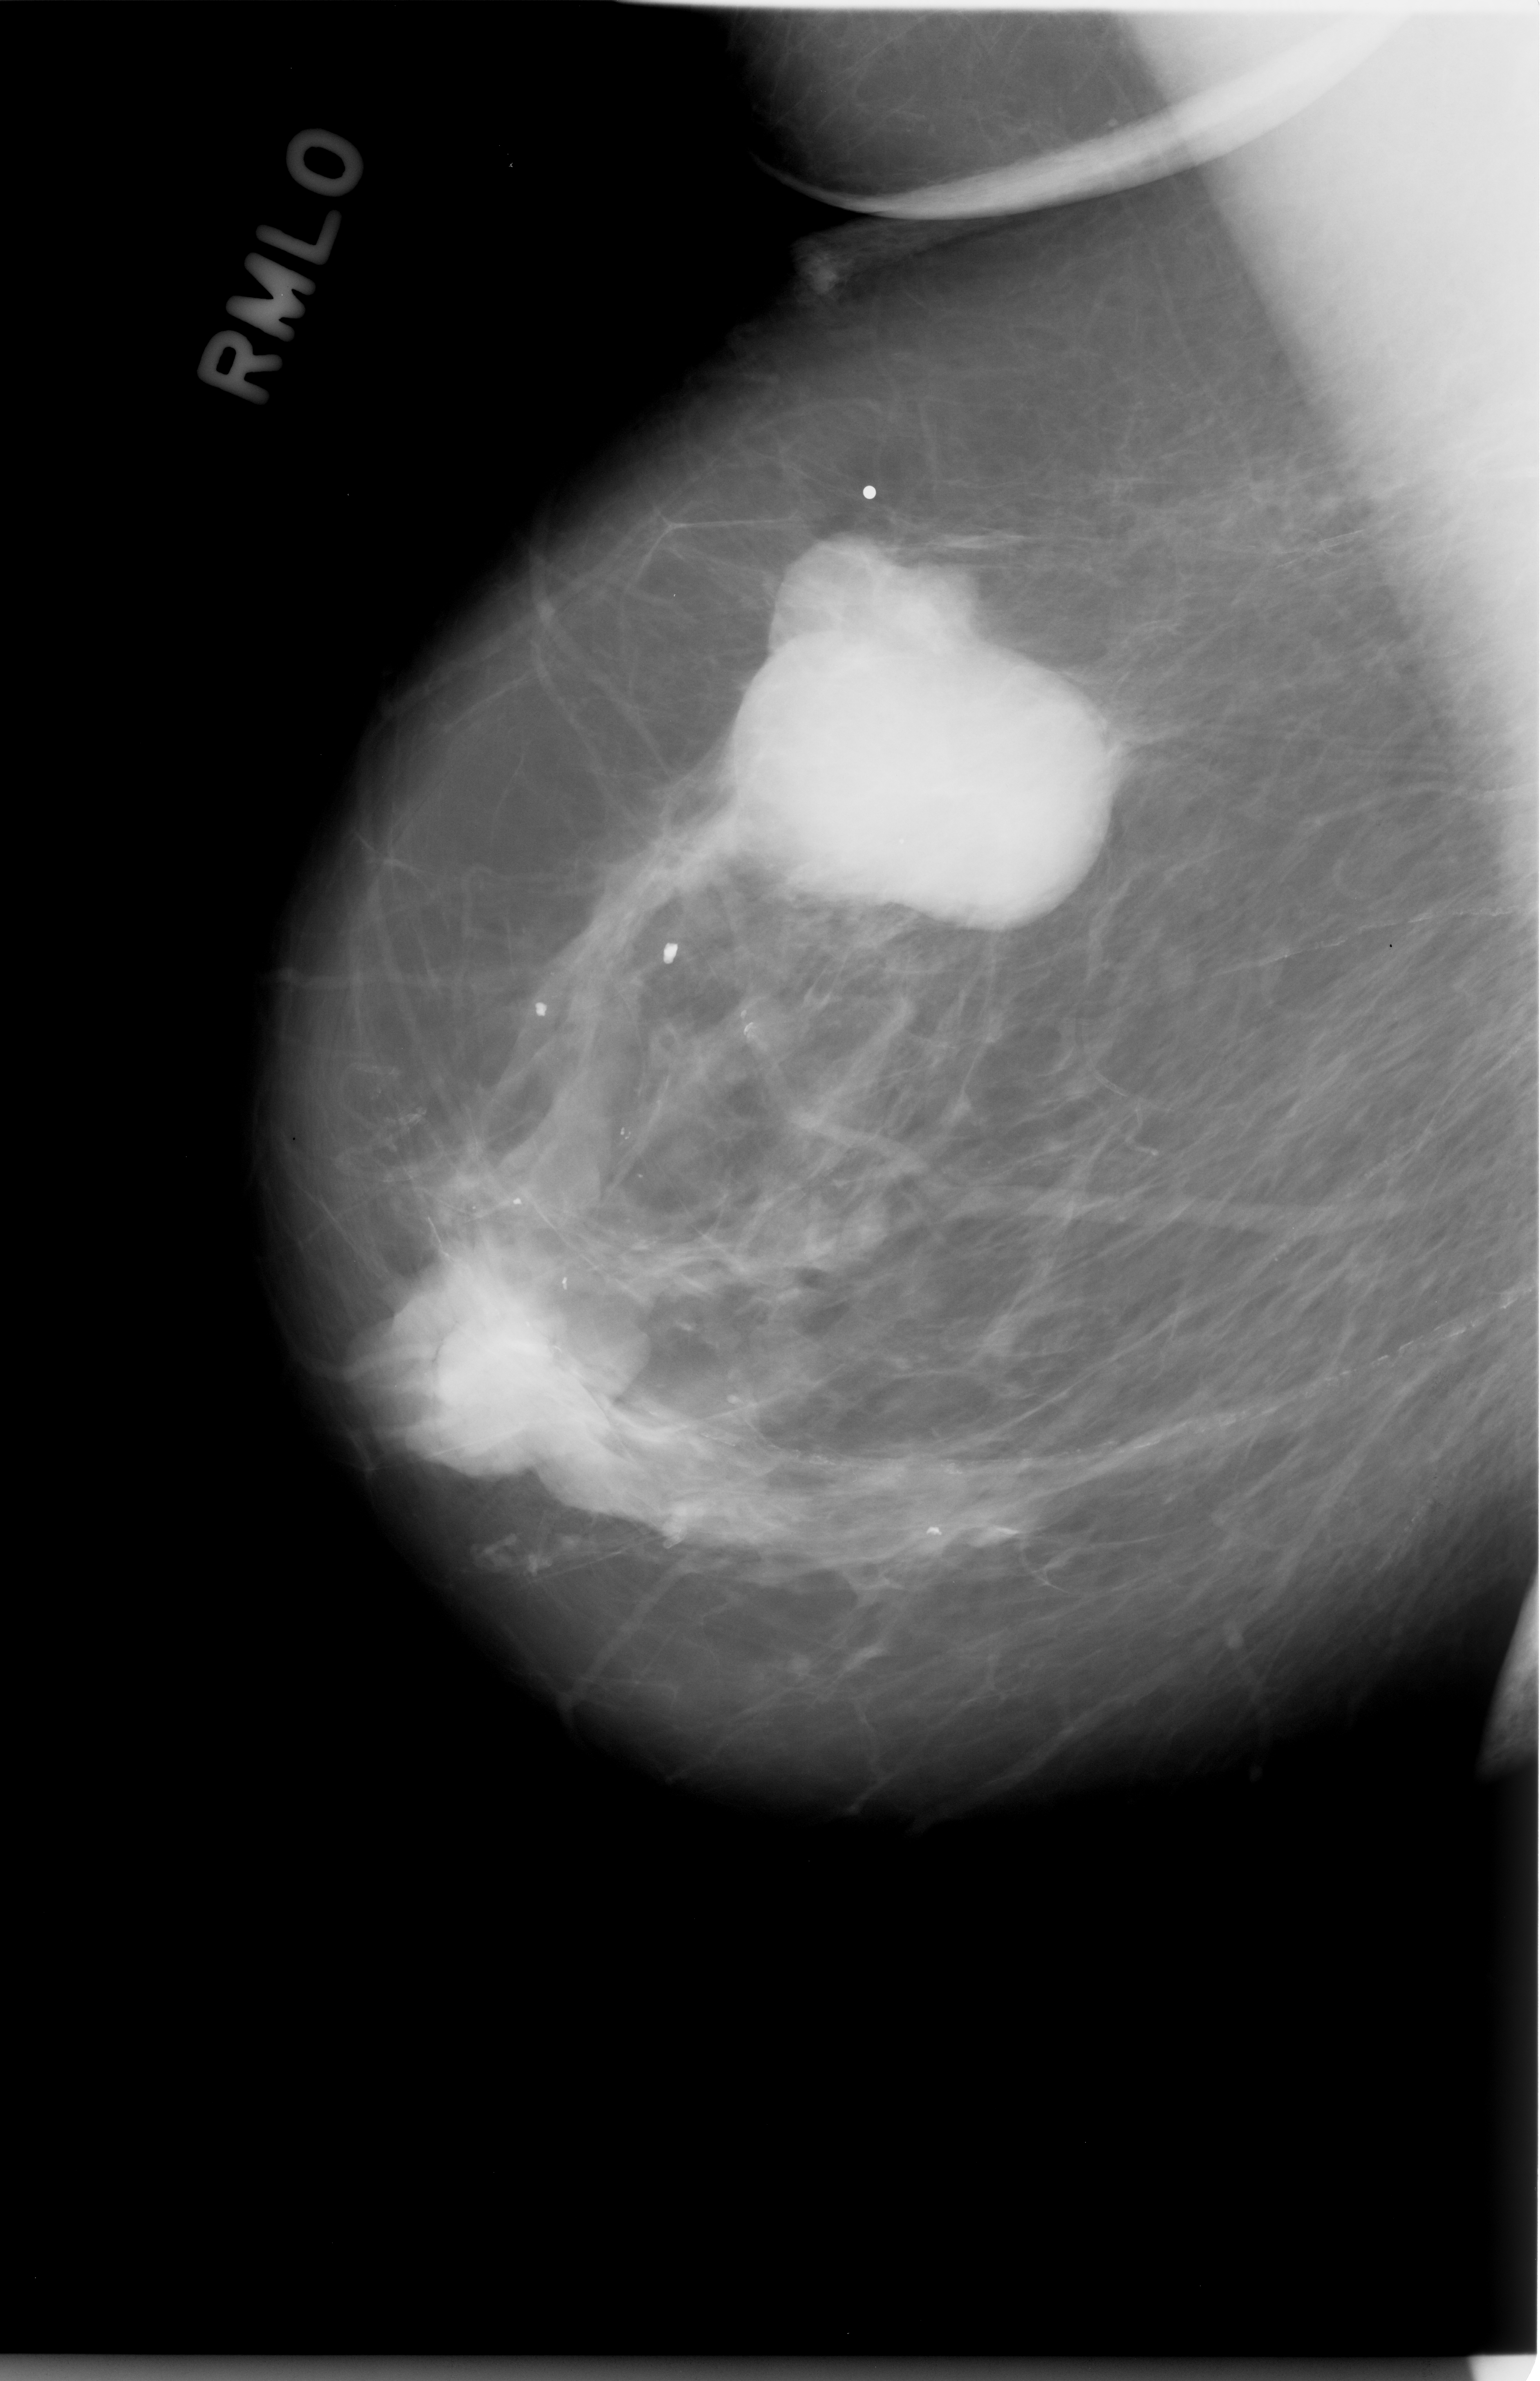
Mammogram (digitized film); right breast; mediolateral oblique (MLO) view; breast composition: almost entirely fatty (BI-RADS density category 1 of 4); 1540 × 2381 image matrix.
Expert-marked regions of interest on this film, with their recorded descriptors:
- Finding 1 of 2: mass, shape lobulated, margins circumscribed; BI-RADS assessment category 5; pathology result (as recorded, not read from the image): malignant: bounding box (x1, y1, x2, y2) in pixels: (343, 1192, 634, 1566)
- Finding 2 of 2: mass, shape lobulated, margins circumscribed; BI-RADS assessment category 5; subtlety rating 5 on a 1 (subtle) to 5 (obvious) scale; pathology result (as recorded, not read from the image): malignant: (738, 566, 1105, 944)